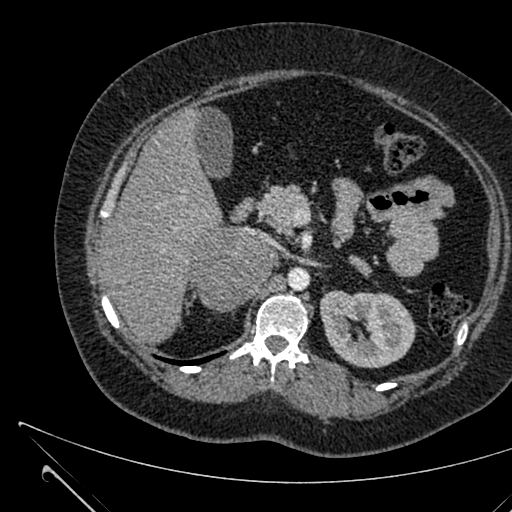
Contrast-enhanced abdominal CT, one axial slice; 120 kVp; soft-tissue window (W 400 / L 40 HU); 1 mm slice thickness; 512 × 512 image matrix. Patient: female, 36 years. From the clinical record (not read from this slice): diagnosis: adrenocortical carcinoma; tumour side: right adrenal; tumour size at pathology: 10 cm; Ki-67 index: 20 %; stage (as recorded): 4.
Structures marked on this image (semi-automatic segmentation, software-assisted and operator-edited):
- mass: box from (x=196, y=233) to (x=275, y=311) px